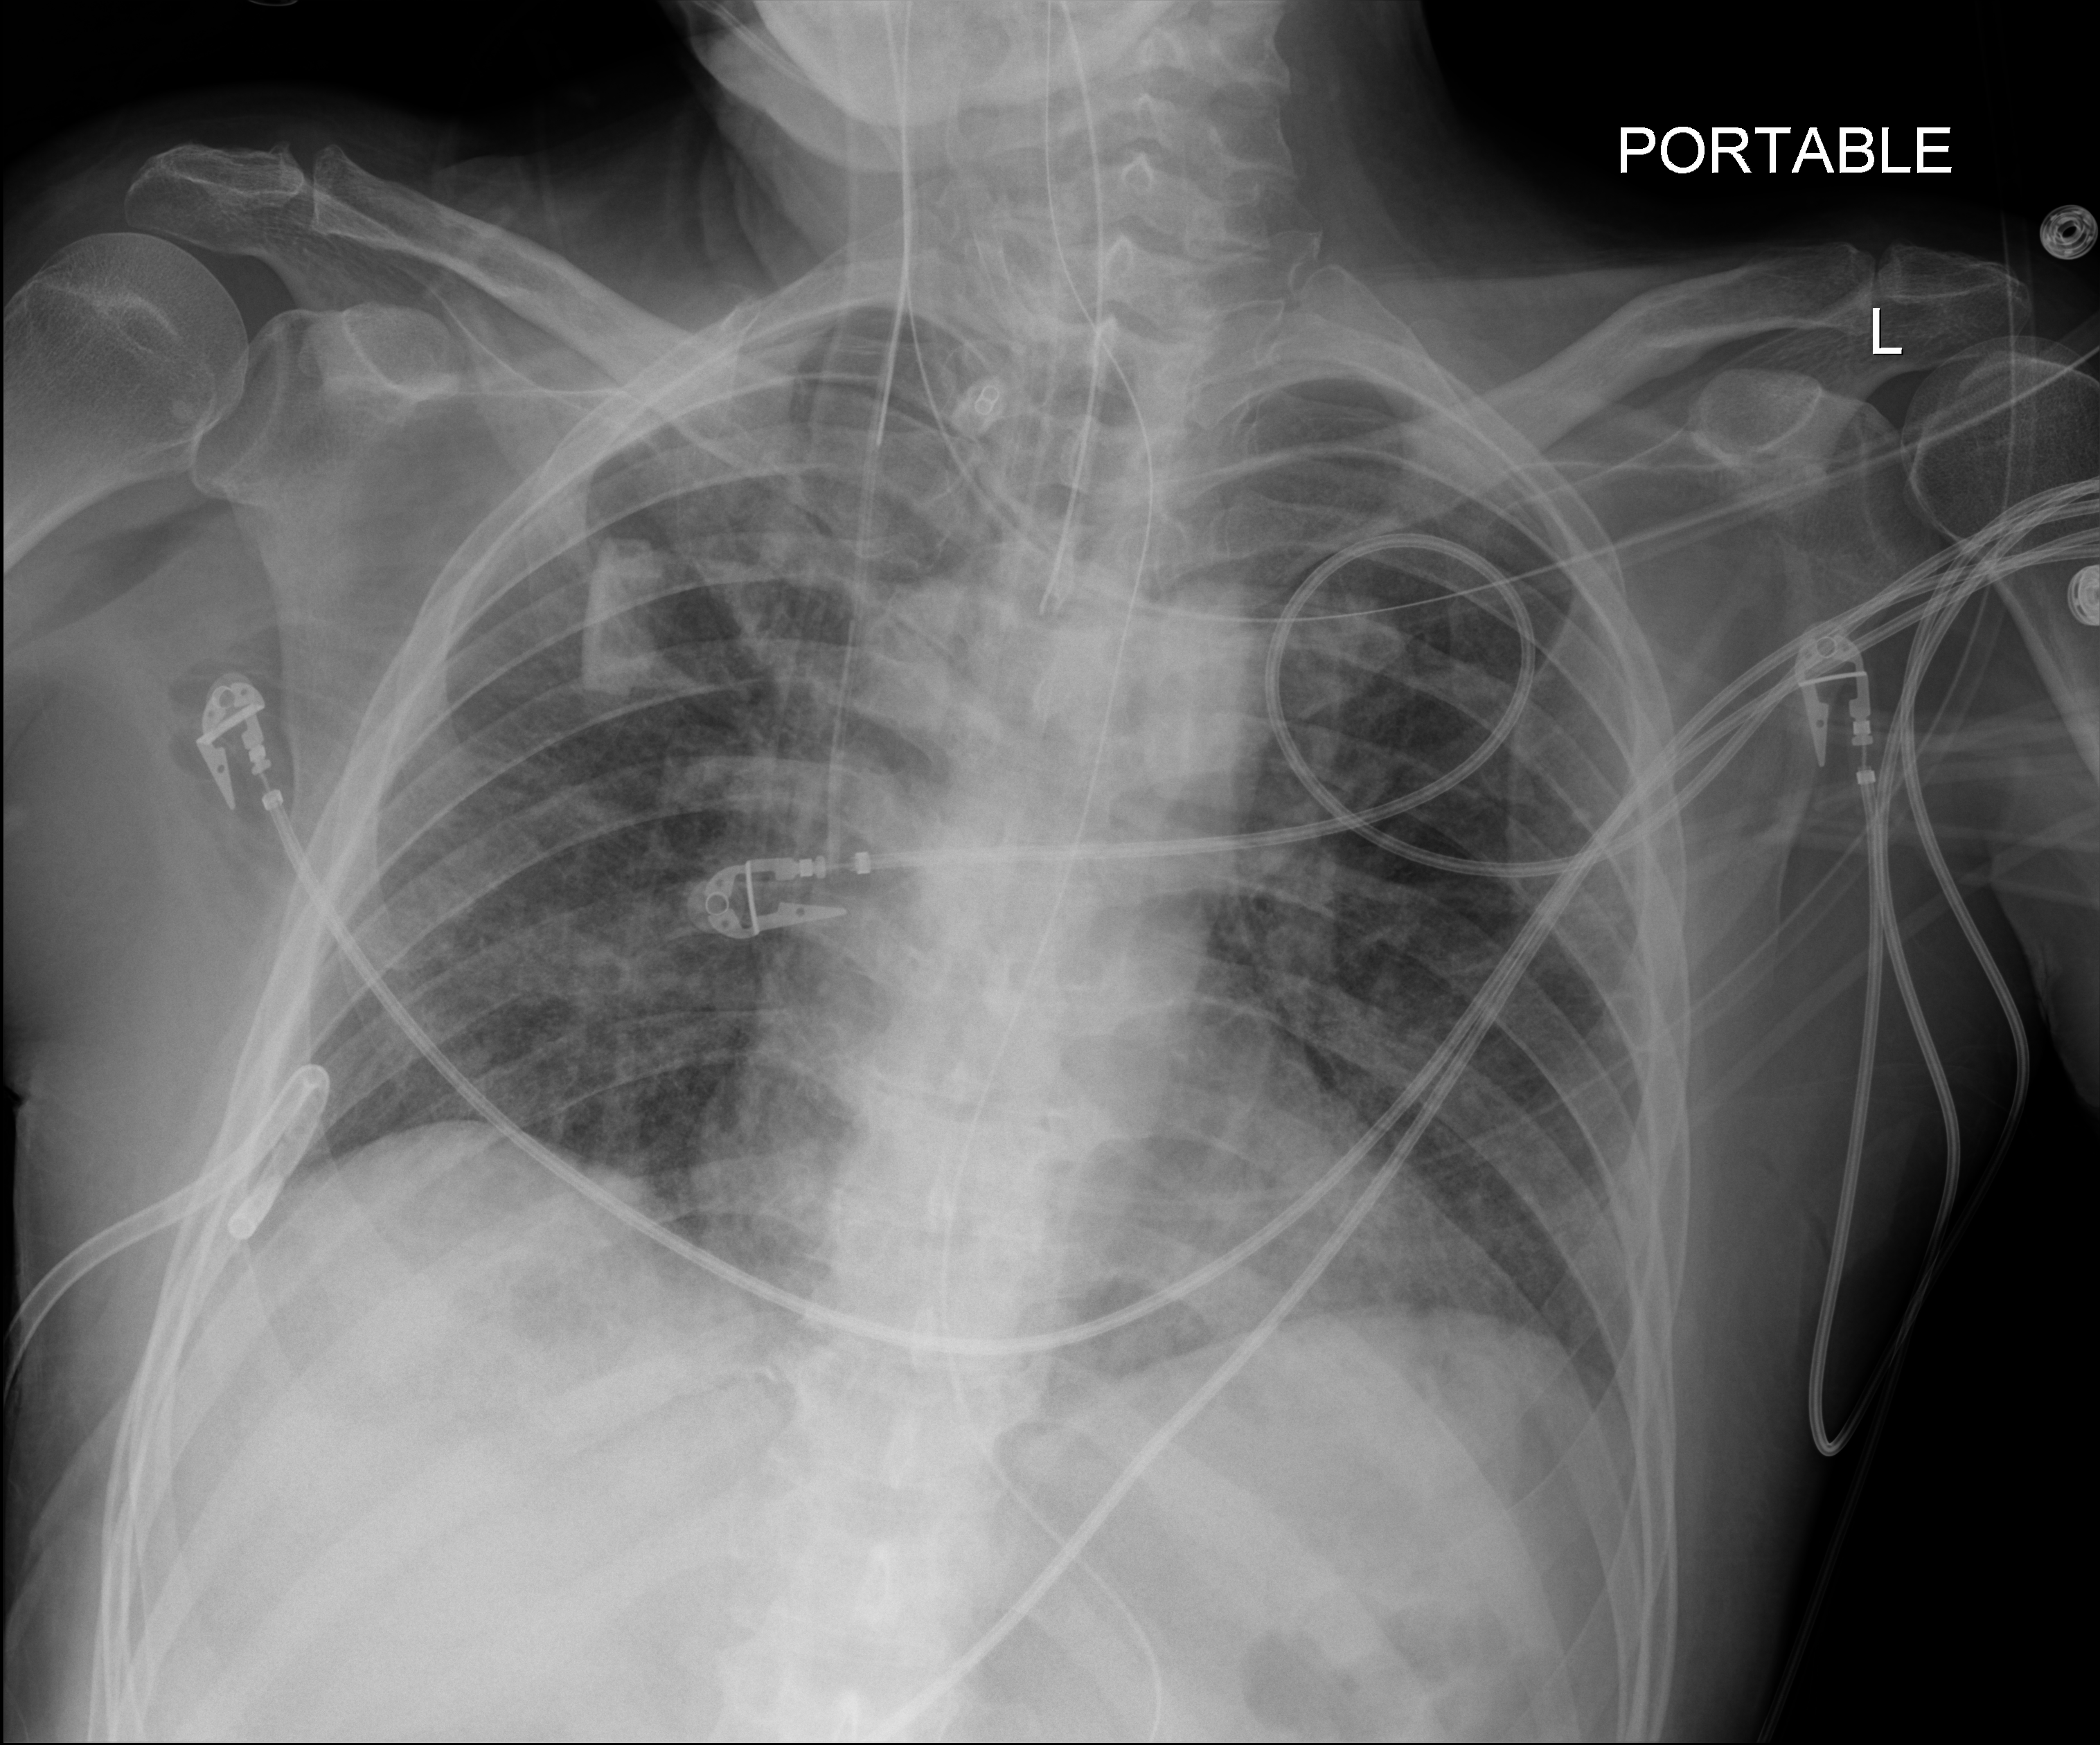
Portable chest radiograph; anteroposterior (AP) projection. Male patient hospitalised with COVID-19, age 18–59 years.
Hospital-stay facts (about this admission, not read from this image; timing relative to this image not recorded): other chronic lung disease (admission record): no; mechanically ventilated during this hospital stay: yes; length of hospital stay: 77 days.